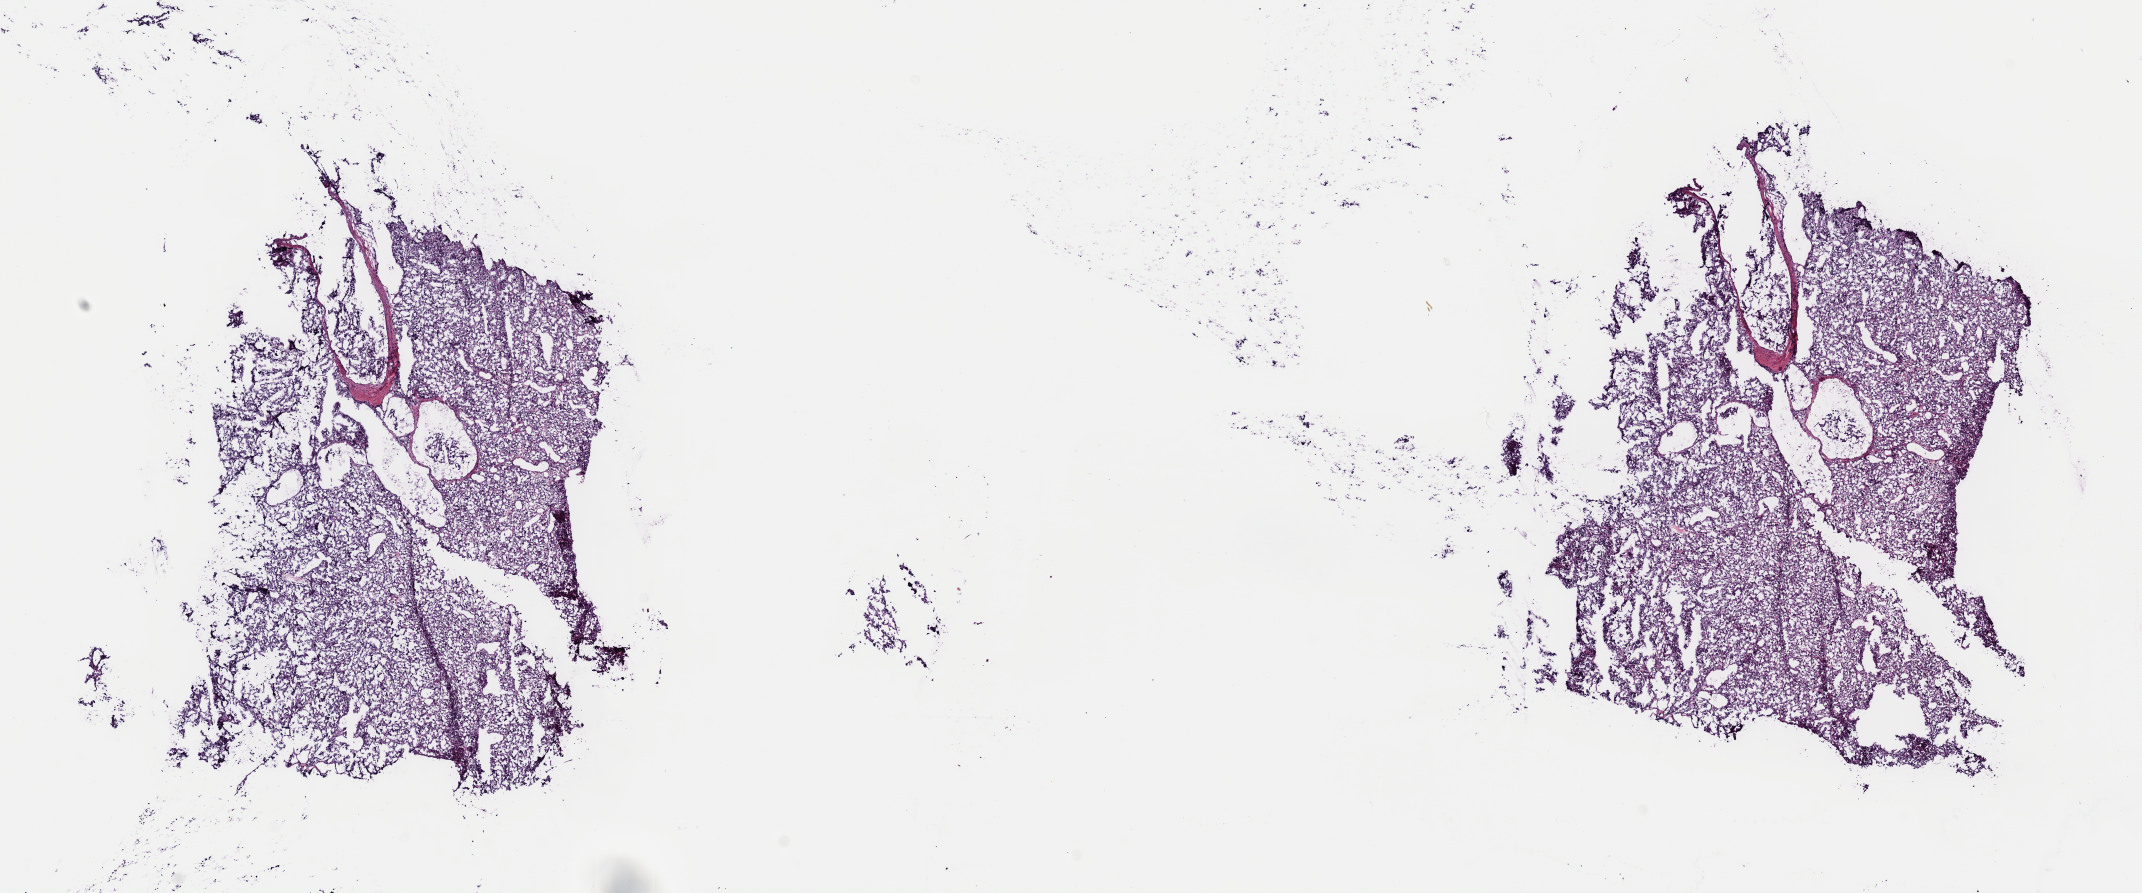
Digitized Hematoxylin and eosin (H&E) stained tissue section (whole slide) — low-resolution overview of the scanned area, about 16.9 x 7.1 mm; frozen section from the top of the tissue portion; retroperitoneum and peritoneum, primary tumour sample. Patient: female, age at initial diagnosis 45 years. Pathologist review of this section (percent, as recorded): tumour cells 100%, tumour nuclei 80%, normal cells 0%, stromal cells 0%, necrosis 0%. Infiltration values recorded for this section: lymphocyte infiltration 1%, monocyte infiltration 0%, neutrophil infiltration 0%.
Histologic diagnosis: Extra-adrenal paraganglioma, NOS (retroperitoneum).